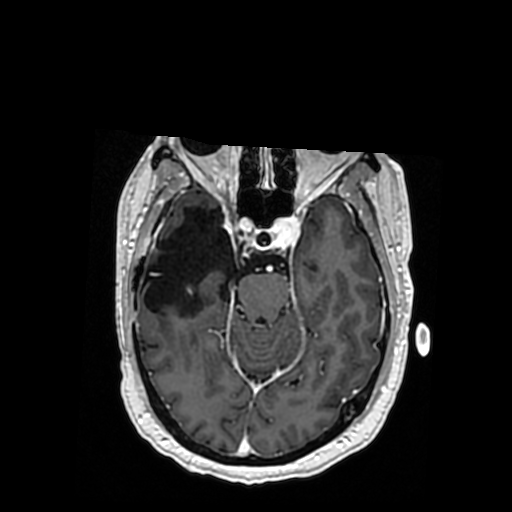
Brain MRI from a brain-tumour surgery series, one axial slice. T1-weighted post-contrast. 0.5 mm slice thickness. 512 × 512 image matrix, field of view 260 × 260 mm. From the clinical record (not read from this slice): histopathology: Oligodendroglioma; WHO grade: 3; IDH mutation: yes; tumour location: Right Posterior Temporal Inferior Parietal.
Annotated regions visible in this slice (manually delineated by an expert):
- previous resection cavity: bounding box (x1, y1, x2, y2) in pixels: (142, 206, 233, 317)